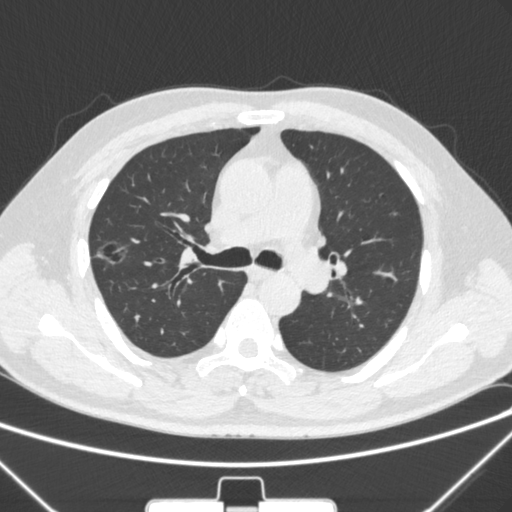
Chest CT, one axial slice. Slice 197 of 320 in the series (ordered by position). Lung window (W 1500 / L -600 HU). 512 × 512 image matrix, field of view 350 × 350 mm. Patient: male, 58 years. From the clinical record (not read from this slice): clinical TNM (as recorded): T1c N0 M0.
Outlined on this slice (bounding box drawn by a radiologist):
- lung tumour (recorded histology: adenocarcinoma): bounding box (x1, y1, x2, y2) in pixels: (89, 229, 134, 276)